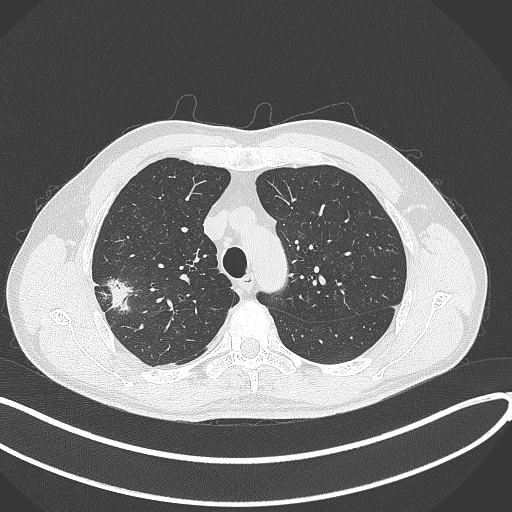
Chest CT, one axial slice; slice 316 of 381 in the series (ordered by position); 120 kVp; lung window (W 1500 / L -600 HU); 1 mm slice thickness; 512 × 512 image matrix, field of view 400 × 400 mm. Patient: male, 62 years. From the clinical record (not read from this slice): clinical TNM (as recorded): T1c N0 M0; histopathological grade: G2-3.
Structures marked on this image (bounding box drawn by a radiologist):
- lung tumour (recorded histology: adenocarcinoma): bounding box (x1, y1, x2, y2) in pixels: (105, 275, 134, 315)